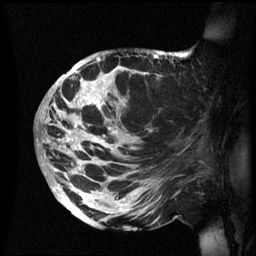
Breast MRI (dynamic contrast-enhanced), one sagittal slice; position 34 of 60 along the scan axis; dynamic contrast-enhanced series, image 2 of 3 at this slice position (ordered by acquisition); 1.5 T; TE 4.2 ms, TR 8.4 ms; 2.4 mm slice thickness; 256 × 256 image matrix, field of view 230 × 230 mm. Patient: female, 48 years.
Annotated regions visible in this slice (semi-automatic segmentation, software-assisted and operator-edited):
- analysis volume of interest (the breast-tissue region the enhancement analysis was run in; not a lesion): bounding box [x1, y1, x2, y2] px = [42, 50, 194, 231]
- tumour enhancement mask (voxels above the 70 % enhancement threshold inside the analysis volume of interest): [43, 52, 179, 217]